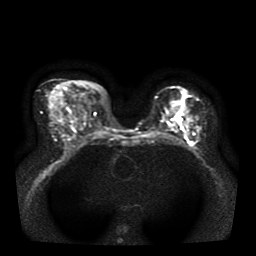
Breast MRI, one axial slice; position 19 of 39 along the scan axis; diffusion-weighted series; image 2 of 4 stored at this slice position (different b-values; order by instance number); 1.5 T; 5 mm slice thickness; 256 × 256 image matrix. Female patient.
Outlined on this slice (outlined manually by an expert reader):
- tumour on diffusion-weighted imaging: box from (x=182, y=109) to (x=191, y=137) px